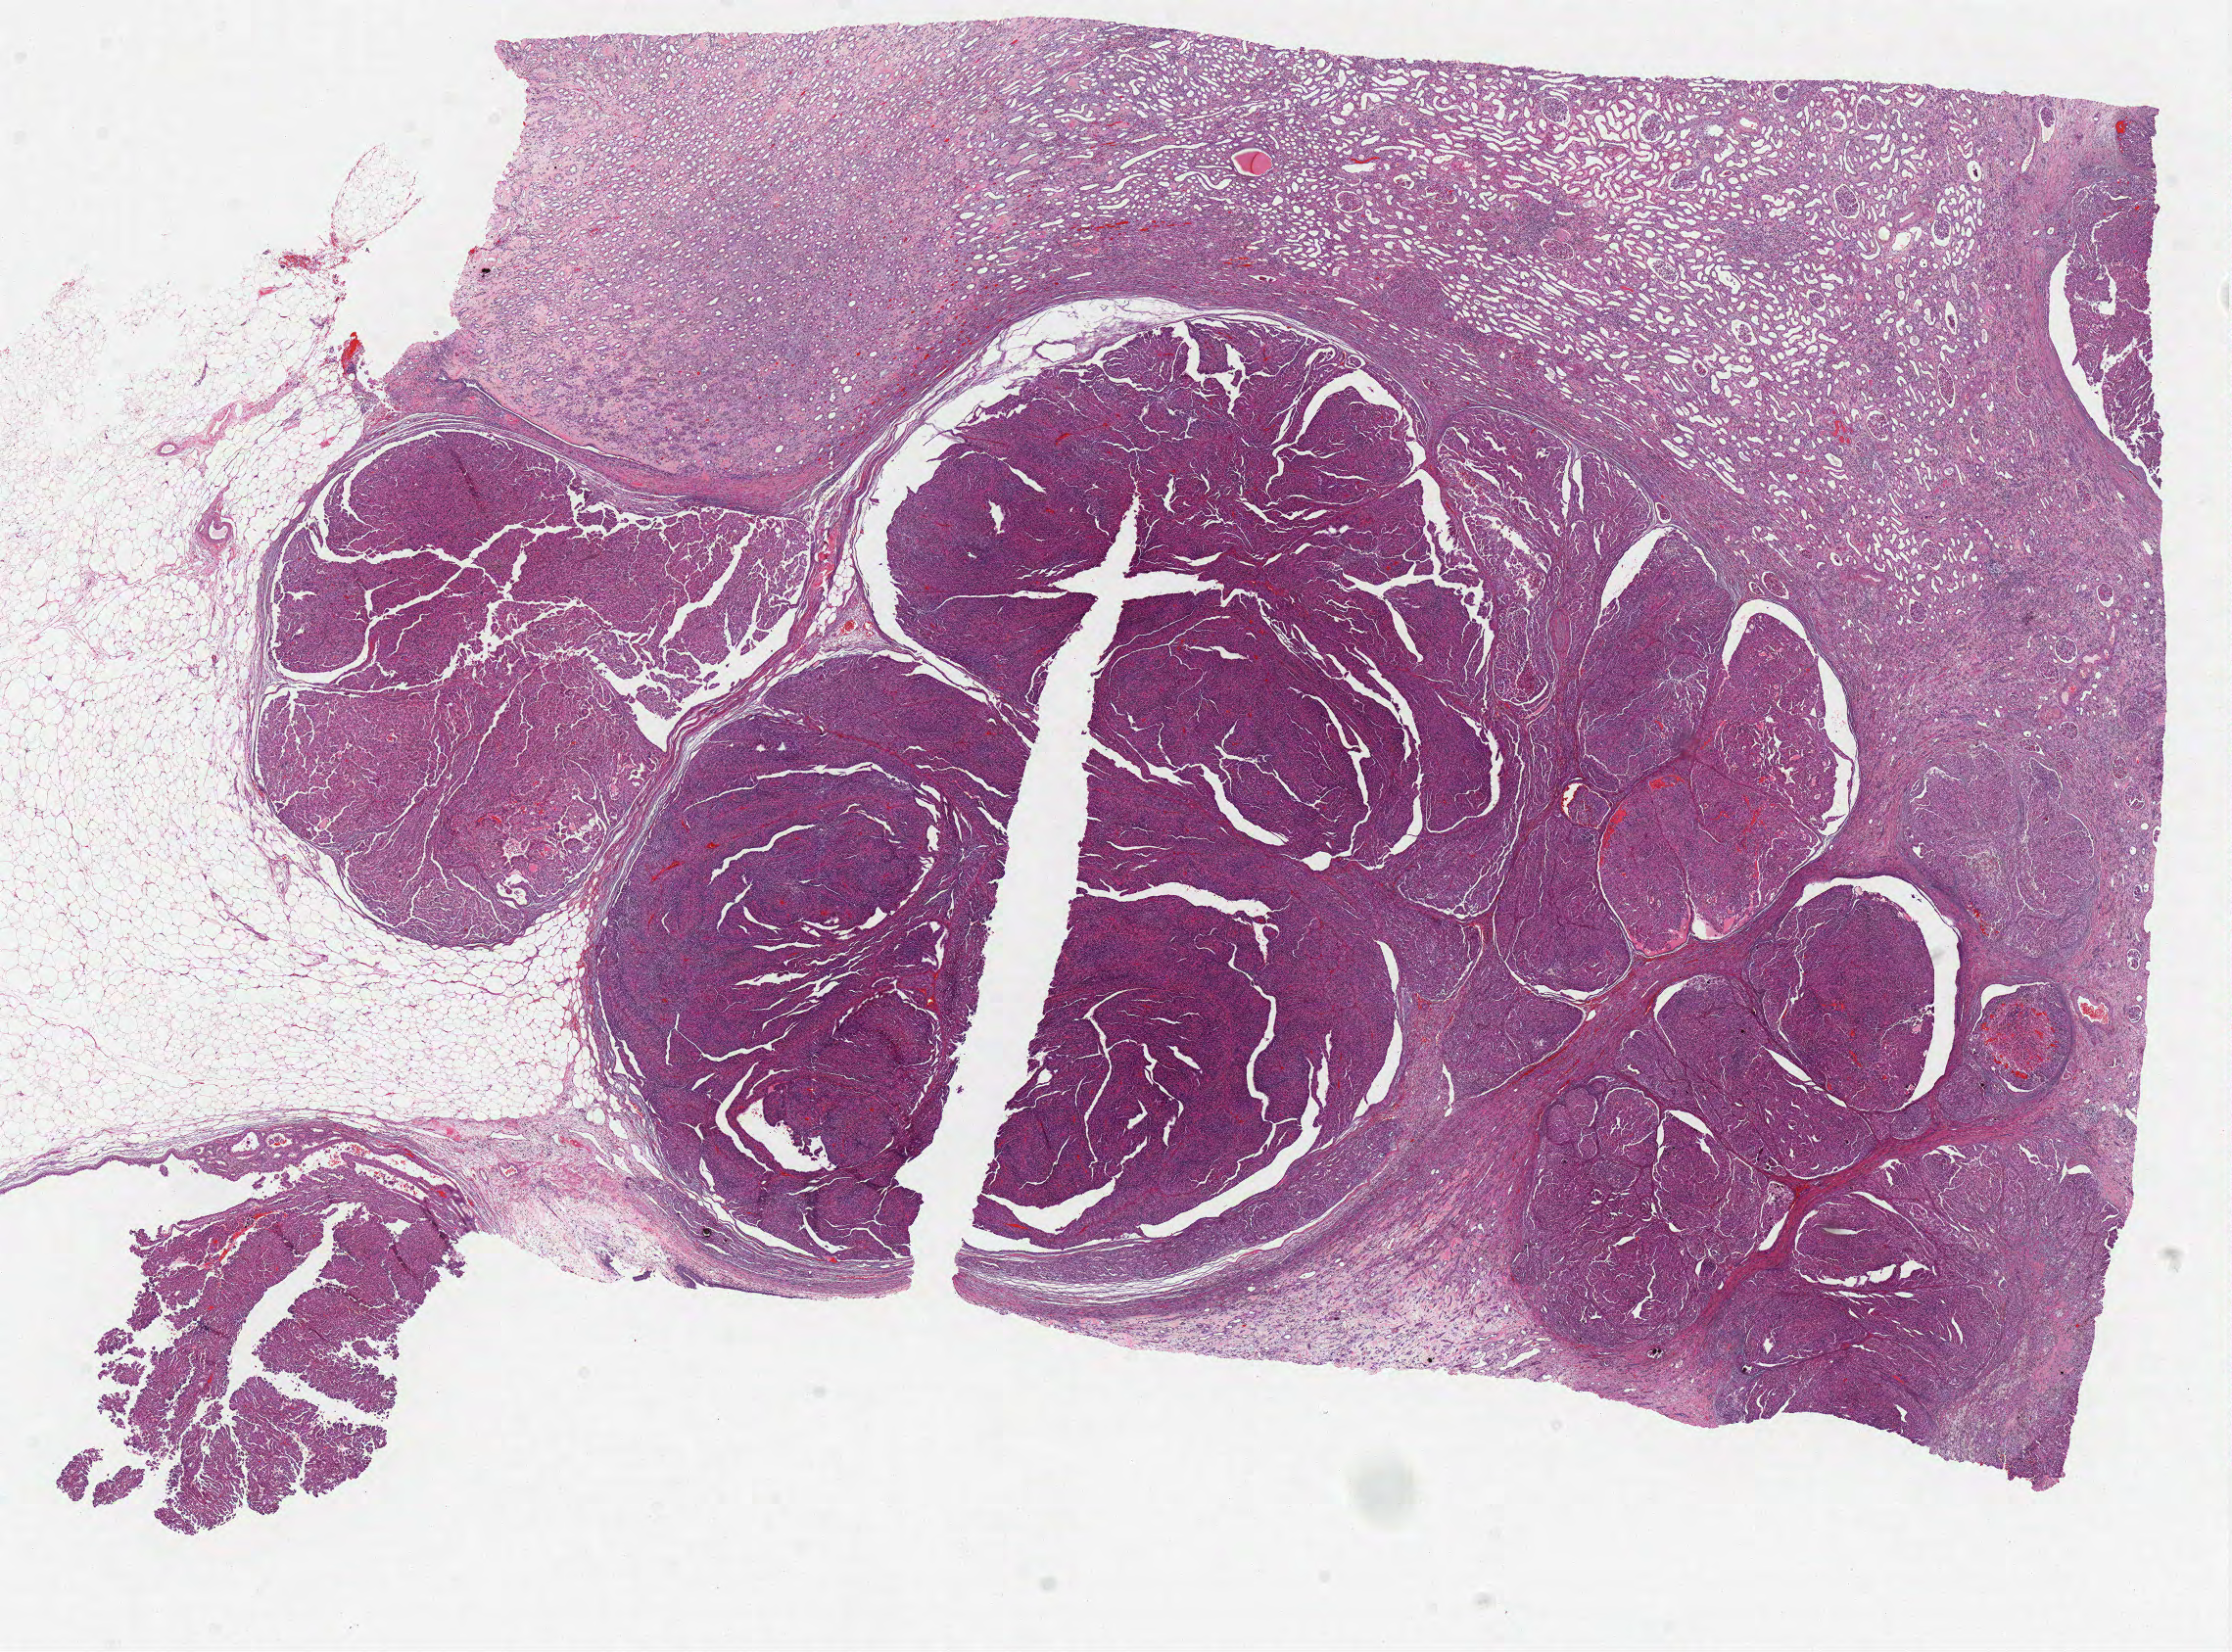
Digitized Hematoxylin and eosin (H&E) stained tissue section (whole slide) — whole scanned area (about 18.2 x 13.5 mm) shown as a low-resolution overview. FFPE section. Kidney, primary tumour sample. Patient: female, age at initial diagnosis 75 years.
Pathologic diagnosis: Papillary adenocarcinoma, NOS.